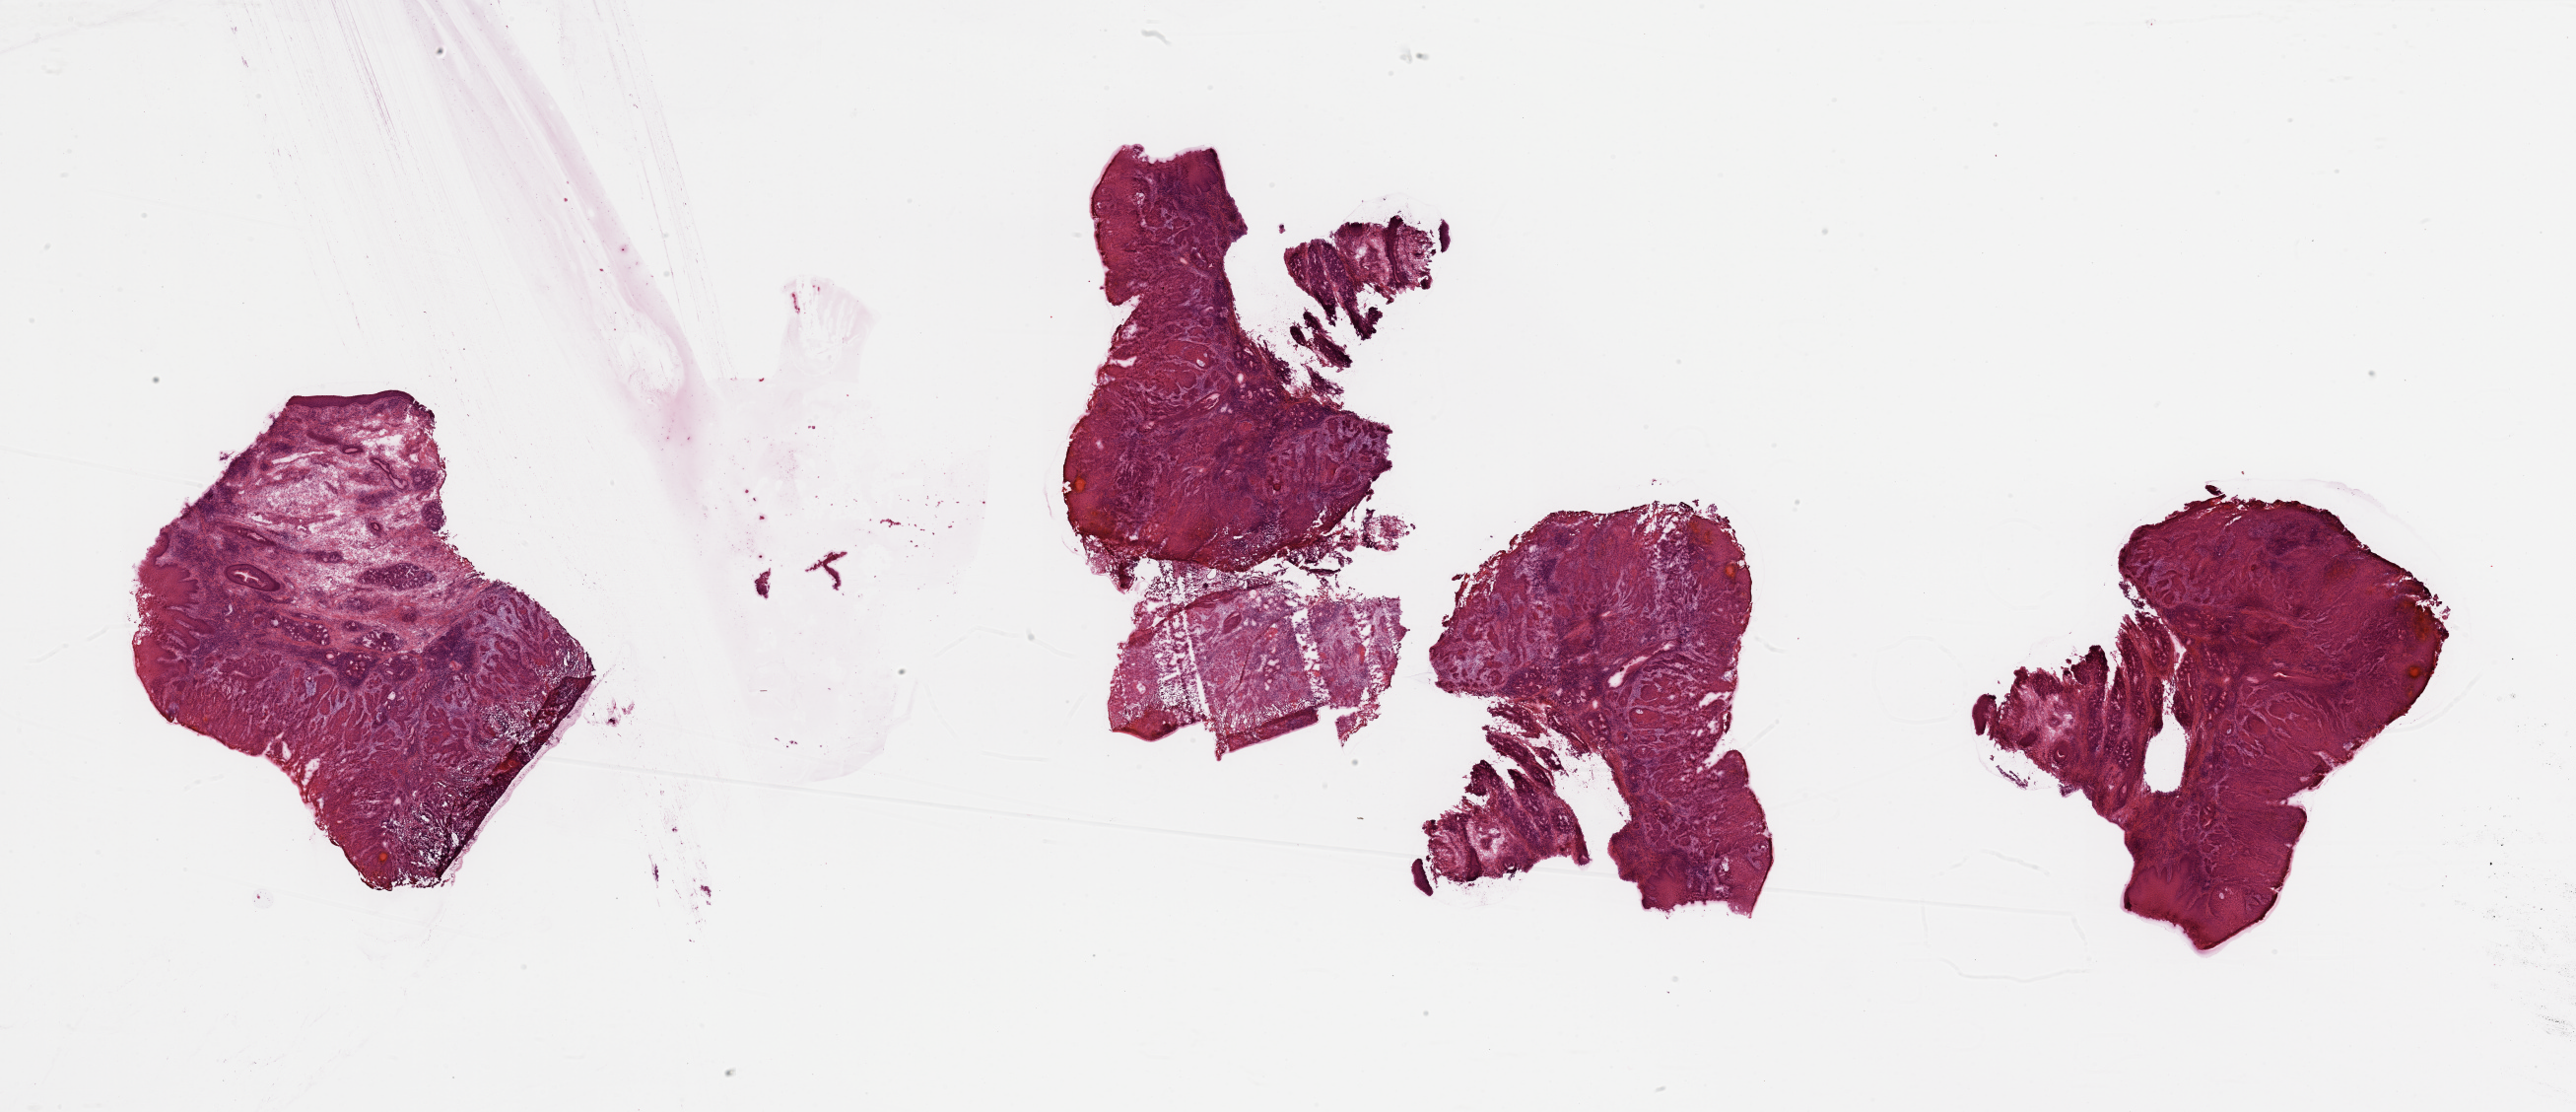
Digitized H&E-stained tissue section (whole slide) — low-resolution overview of the scanned area, about 41.3 x 17.8 mm (slide scanned at 20x). Tumour tissue sample, sampled site: larynx. 53-year-old female patient. Pathologist review of this section (percent, as recorded): tumour nuclei 90%, necrosis 5%.
Diagnosis: Squamous cell carcinoma, NOS.